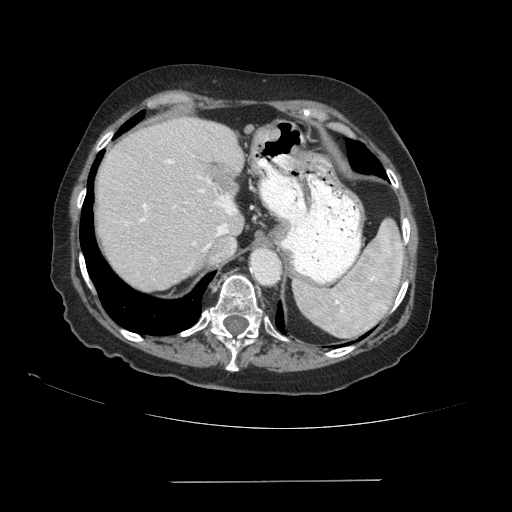
Contrast-enhanced abdominal CT (liver protocol), one axial slice. Position 69 of 89 along the scan axis. 140 kVp. Soft-tissue window (W 400 / L 40 HU). 2.5 mm slice thickness. 512 × 512 image matrix, field of view 400 × 400 mm. Case-level facts recorded for this patient, not image findings: diagnosis: hepatocellular carcinoma (patient treated with transarterial chemoembolisation; whether this scan precedes or follows treatment is not stated here); TNM stage (as recorded): Stage-IVA; Child-Pugh class: A; tumour differentiation: poorly differentiated; tumour nodularity: uninodular.
Outlined on this slice (semi-automatically segmented with operator editing):
- abdominal aorta: box from (x=252, y=250) to (x=277, y=281) px
- liver parenchyma outside the tumour (the mass and vessels are separate outlines, so this box may not span the whole liver): (x=96, y=118)–(x=244, y=290)
- liver vessels: (x=126, y=159)–(x=236, y=251)